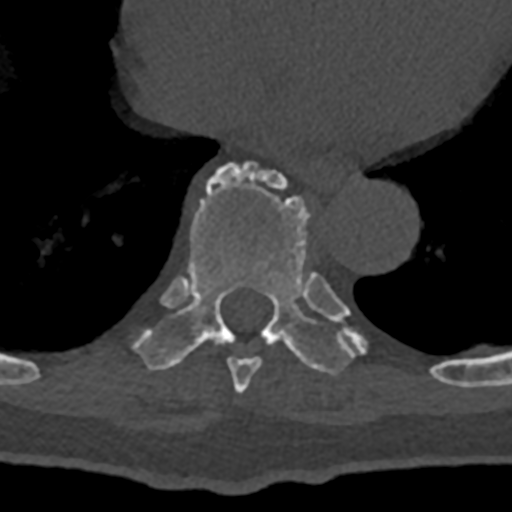
CT including the spine, one axial slice. Position 672 of 797 along the scan axis. Reconstruction kernel Br40s/3. Bone window (W 1800 / L 400 HU). 512 × 512 image matrix, field of view 160 × 160 mm. Patient: male, 74 years. Case-level facts recorded for this patient, not image findings: primary cancer: renal.
Outlined on this slice (semi-automatically segmented with operator editing):
- T8 vertebra: bounding box <227,357,262,393> (left, top, right, bottom; pixels)
- T9 vertebra: <132,163,432,375>